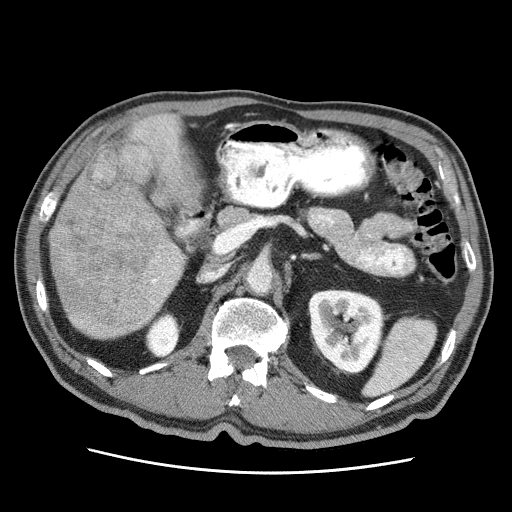
Contrast-enhanced abdominal CT (liver protocol), one axial slice. Position 18 of 75 along the scan axis. Reconstruction kernel STANDARD. 120 kVp. Soft-tissue window (W 400 / L 40 HU). 512 × 512 image matrix. Case-level facts recorded for this patient, not image findings: diagnosis: hepatocellular carcinoma (patient treated with transarterial chemoembolisation; whether this scan precedes or follows treatment is not stated here); TNM stage (as recorded): Stage-IIIA; Child-Pugh class: A; tumour differentiation: well differentiated.
Annotated regions visible in this slice (semi-automatically segmented with operator editing):
- liver parenchyma outside the tumour (the mass and vessels are separate outlines, so this box may not span the whole liver): bounding box [x1, y1, x2, y2] px = [48, 113, 198, 338]
- mass: [51, 145, 157, 324]
- liver vessels: [150, 128, 179, 304]